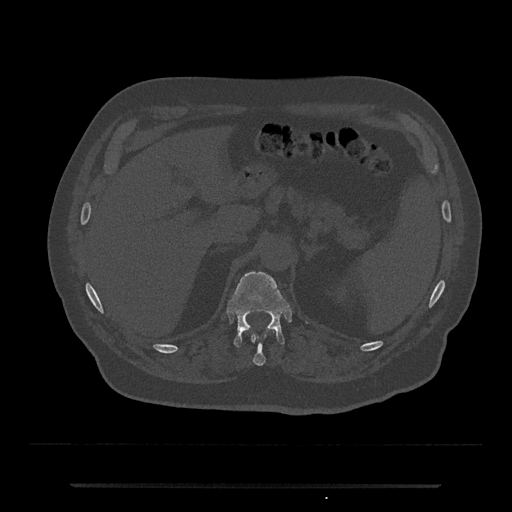
CT including the spine, one axial slice; position 612 of 797 along the scan axis; bone window (W 1800 / L 400 HU); 512 × 512 image matrix, field of view 434 × 434 mm. Patient: male, 80 years. Case-level facts recorded for this patient, not image findings: primary cancer: prostate; vertebrae with lytic lesions (as recorded): L1, T11.
Outlined on this slice (semi-automatically segmented with operator editing):
- T11 vertebra: bounding box (x1, y1, x2, y2) in pixels: (251, 335, 266, 366)
- T12 vertebra: (228, 271, 289, 347)